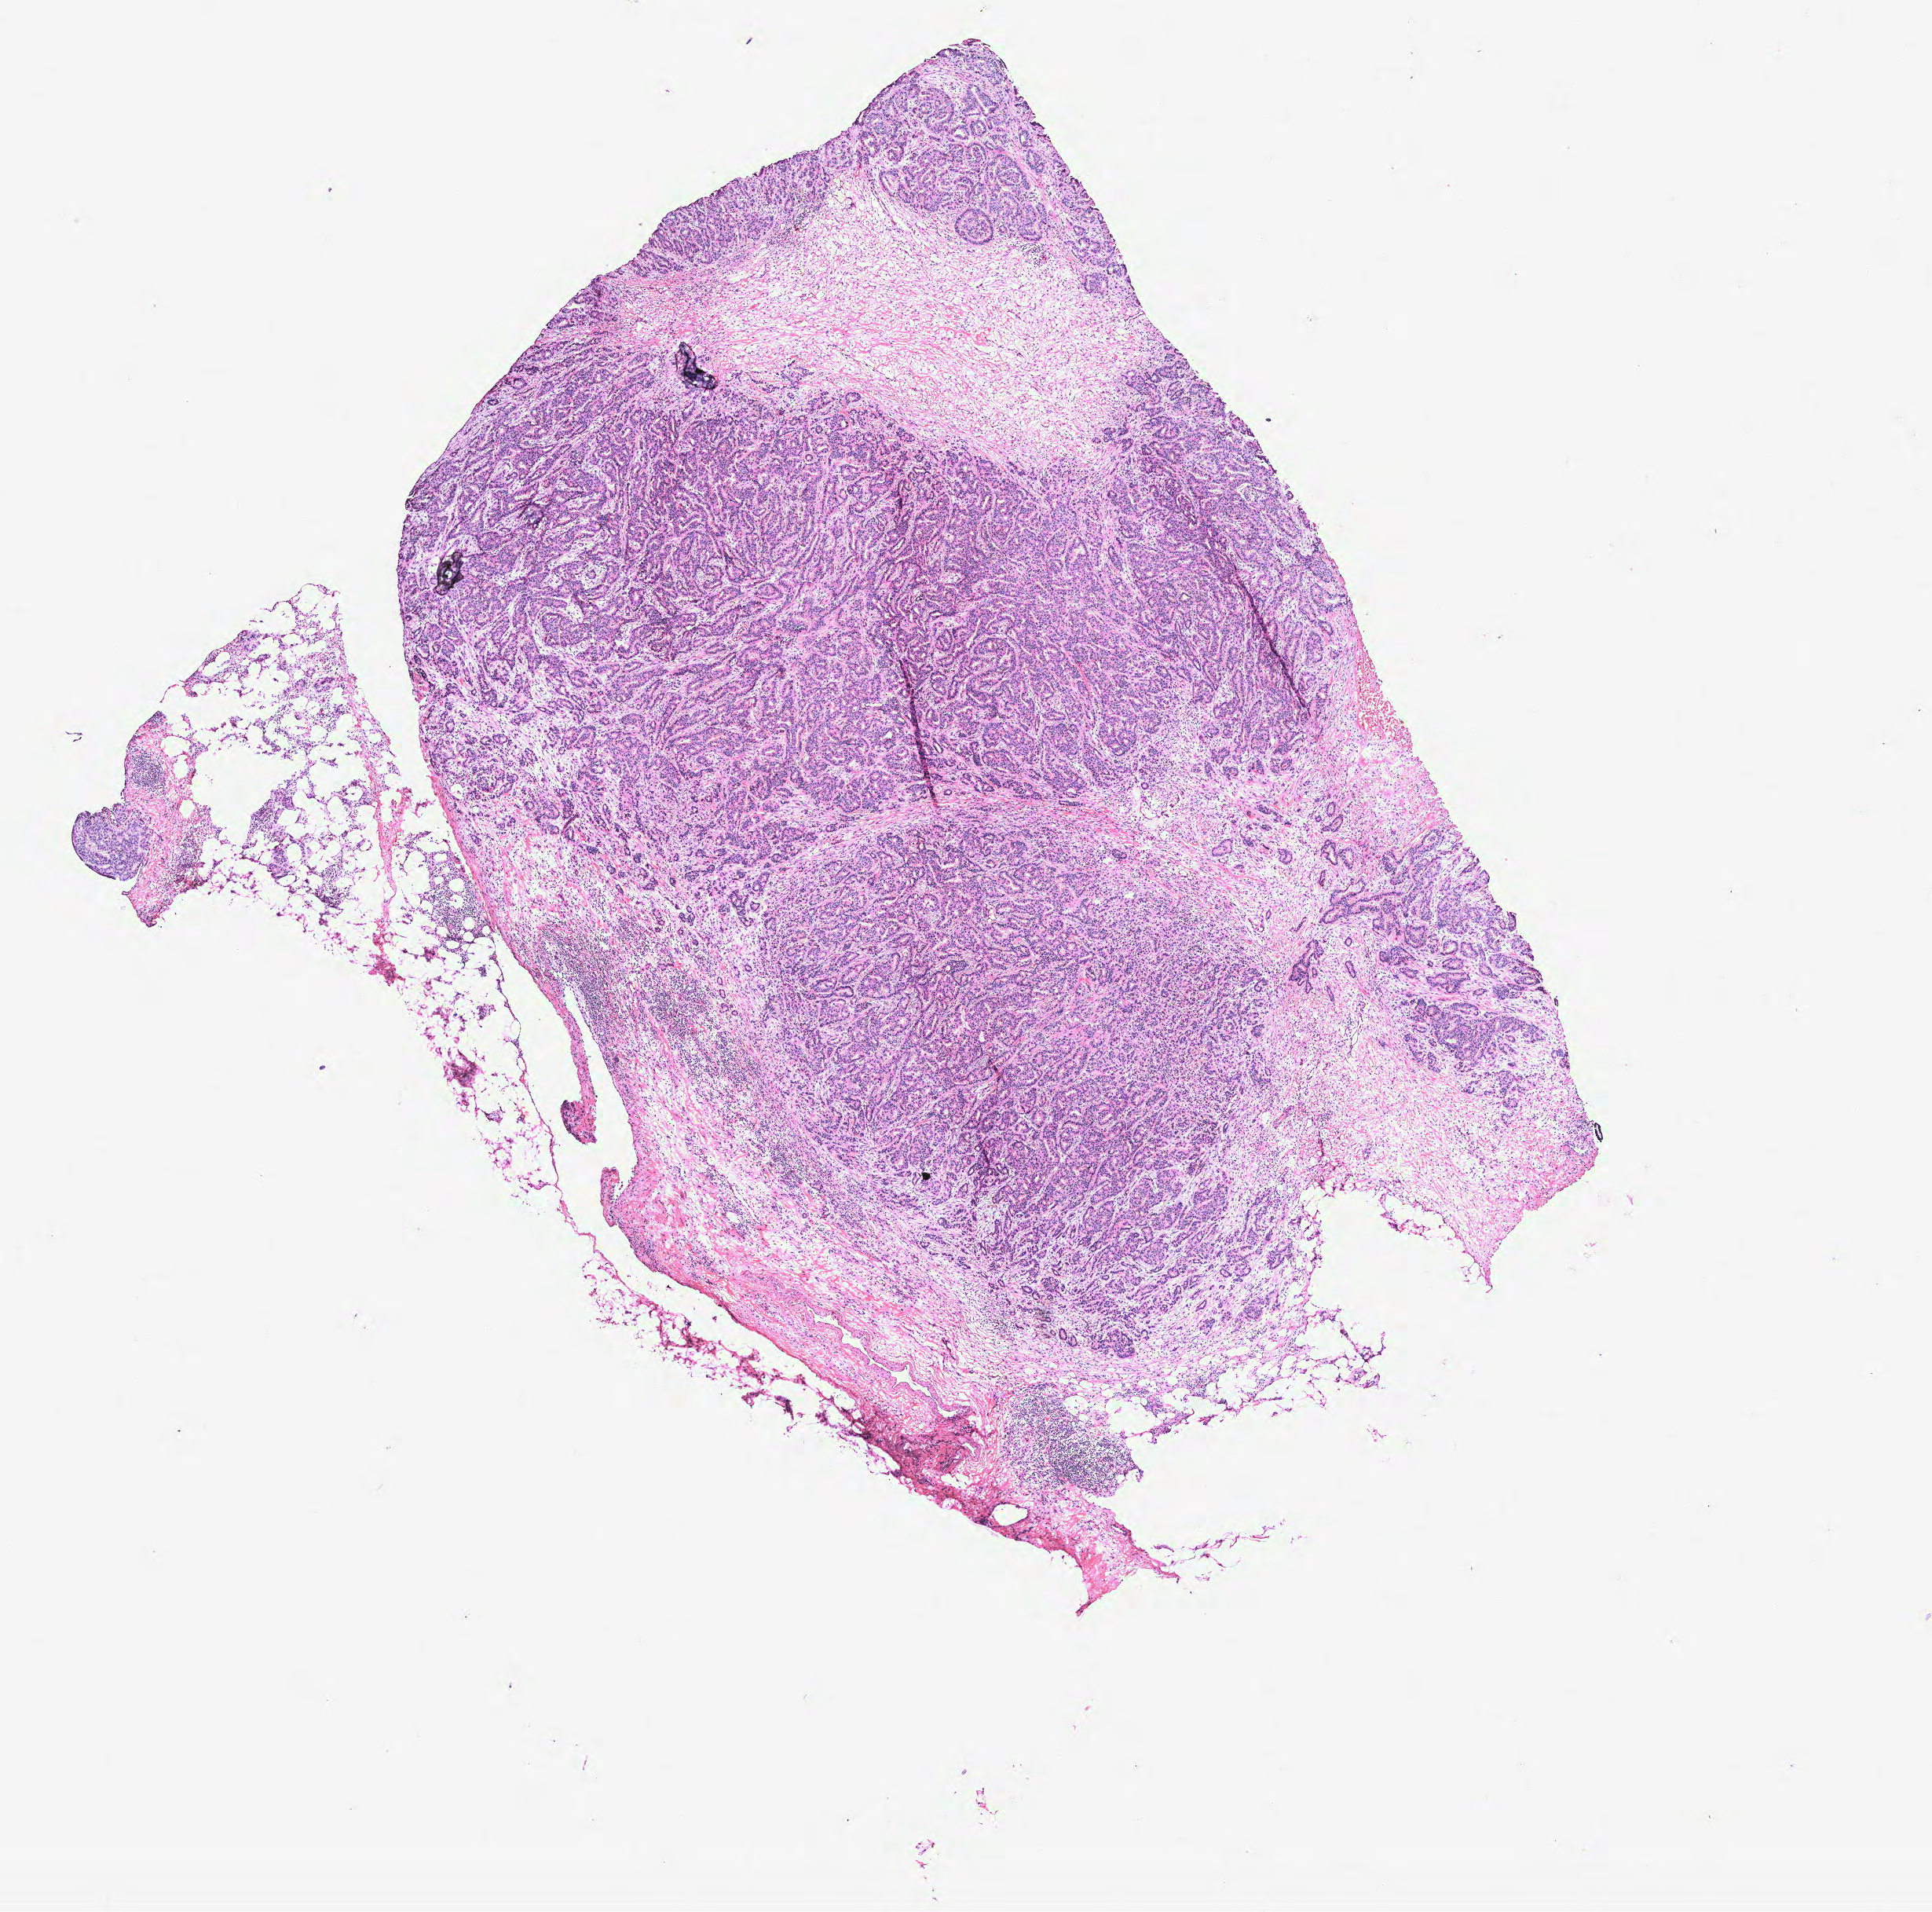
H&E-stained whole-slide image, low-resolution overview of the scanned area, about 9.8 x 9.7 mm (acquisition: 40x scan). Breast, tumour tissue. 55-year-old female patient.
• histologic diagnosis: Infiltrating duct carcinoma, NOS
• AJCC pathologic stage: IIIA